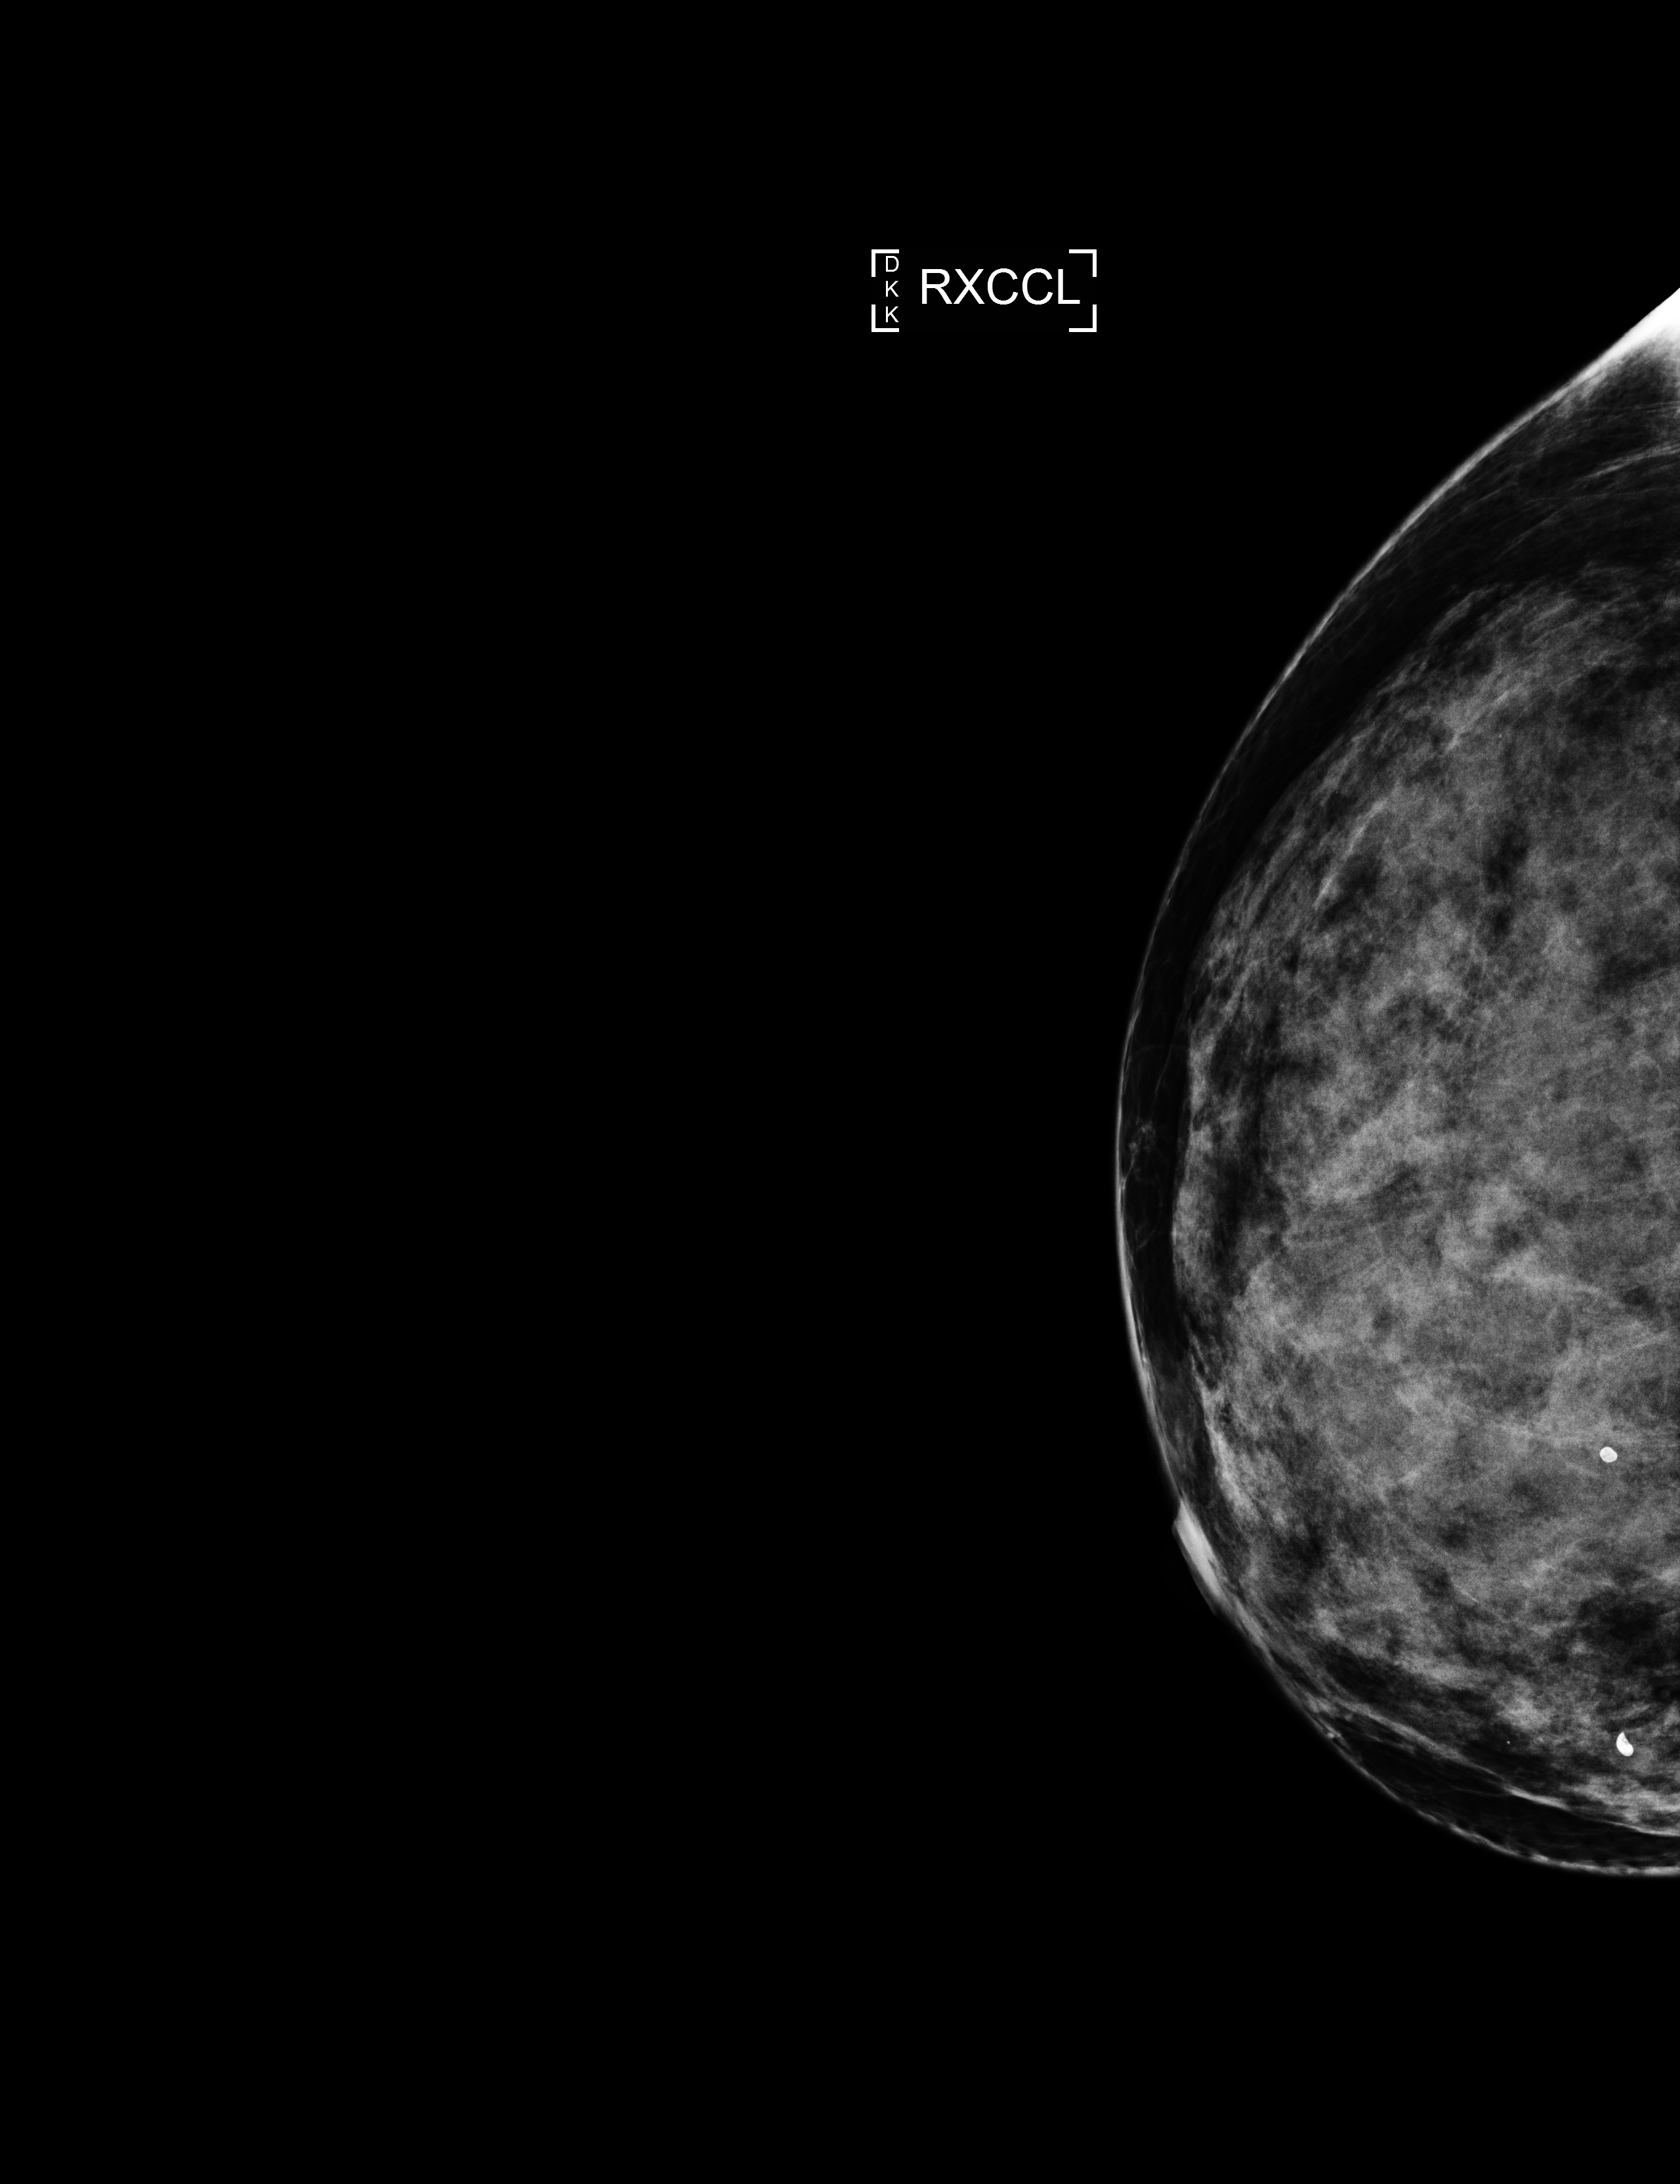
Screening examination. Patient aged 63 years (female).
Image type: full-field digital mammogram. Breast: right. Projection: laterally exaggerated craniocaudal (XCCL) view.